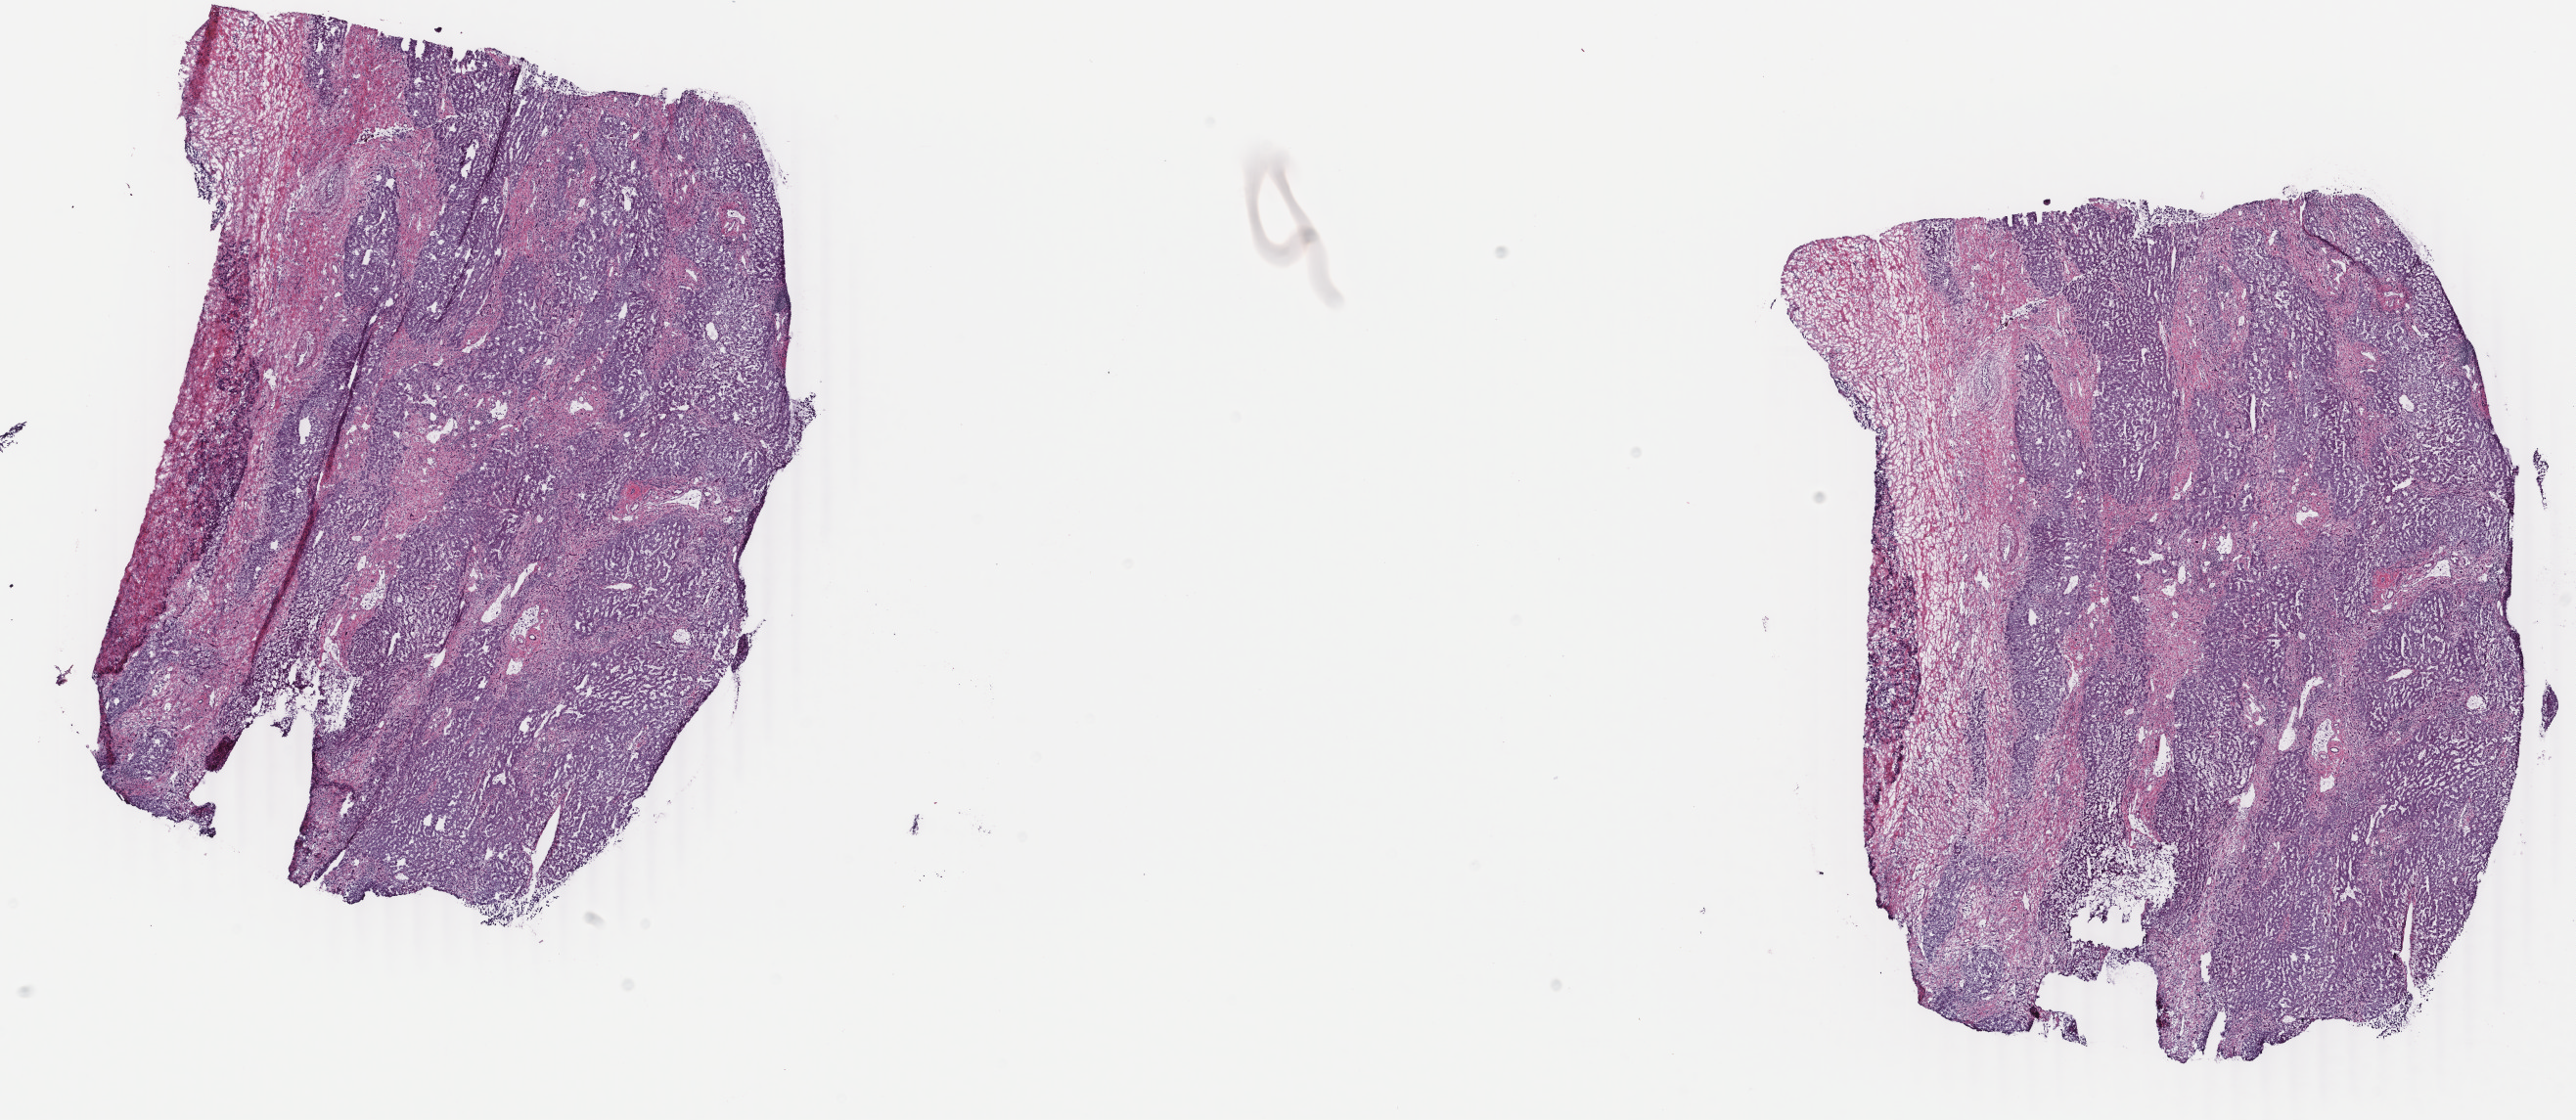
Whole-slide histology image, Hematoxylin and eosin (H&E) stained — shown as a low-resolution overview of the whole scanned area (about 20.9 x 9.1 mm). Frozen section from the bottom of the tissue portion. Sample: primary tumour, liver. Female patient; age at initial diagnosis 51 years. Histologic grade: G1 (well differentiated). Composition of this section per pathologist review: tumour cells 55%, tumour nuclei 55%, normal cells 0%, stromal cells 45%, necrosis 0%. Inflammatory infiltration, as recorded: lymphocyte infiltration 10%, monocyte infiltration 0%, neutrophil infiltration 0%.
Histologic diagnosis: Hepatocellular carcinoma, NOS.